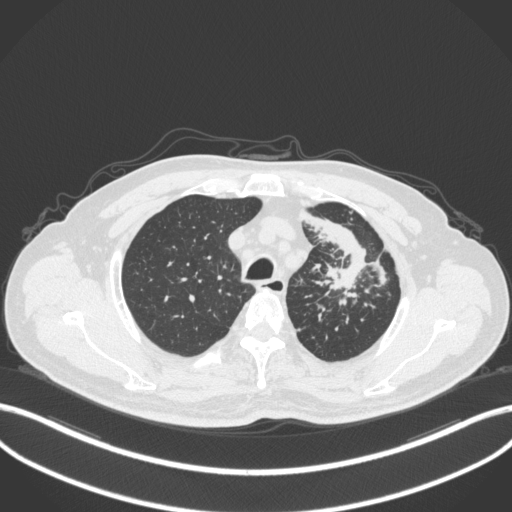
Chest CT, one axial slice. Slice 287 of 386 in the series (ordered by position). Reconstruction kernel B31f. Lung window (W 1500 / L -600 HU). 1 mm slice thickness. 512 × 512 image matrix. Patient: male, 69 years. From the clinical record (not read from this slice): clinical TNM (as recorded): T2a N2 M0.
Outlined on this slice (bounding box drawn by a radiologist):
- lung tumour (recorded histology: adenocarcinoma): box from (x=301, y=207) to (x=372, y=296) px